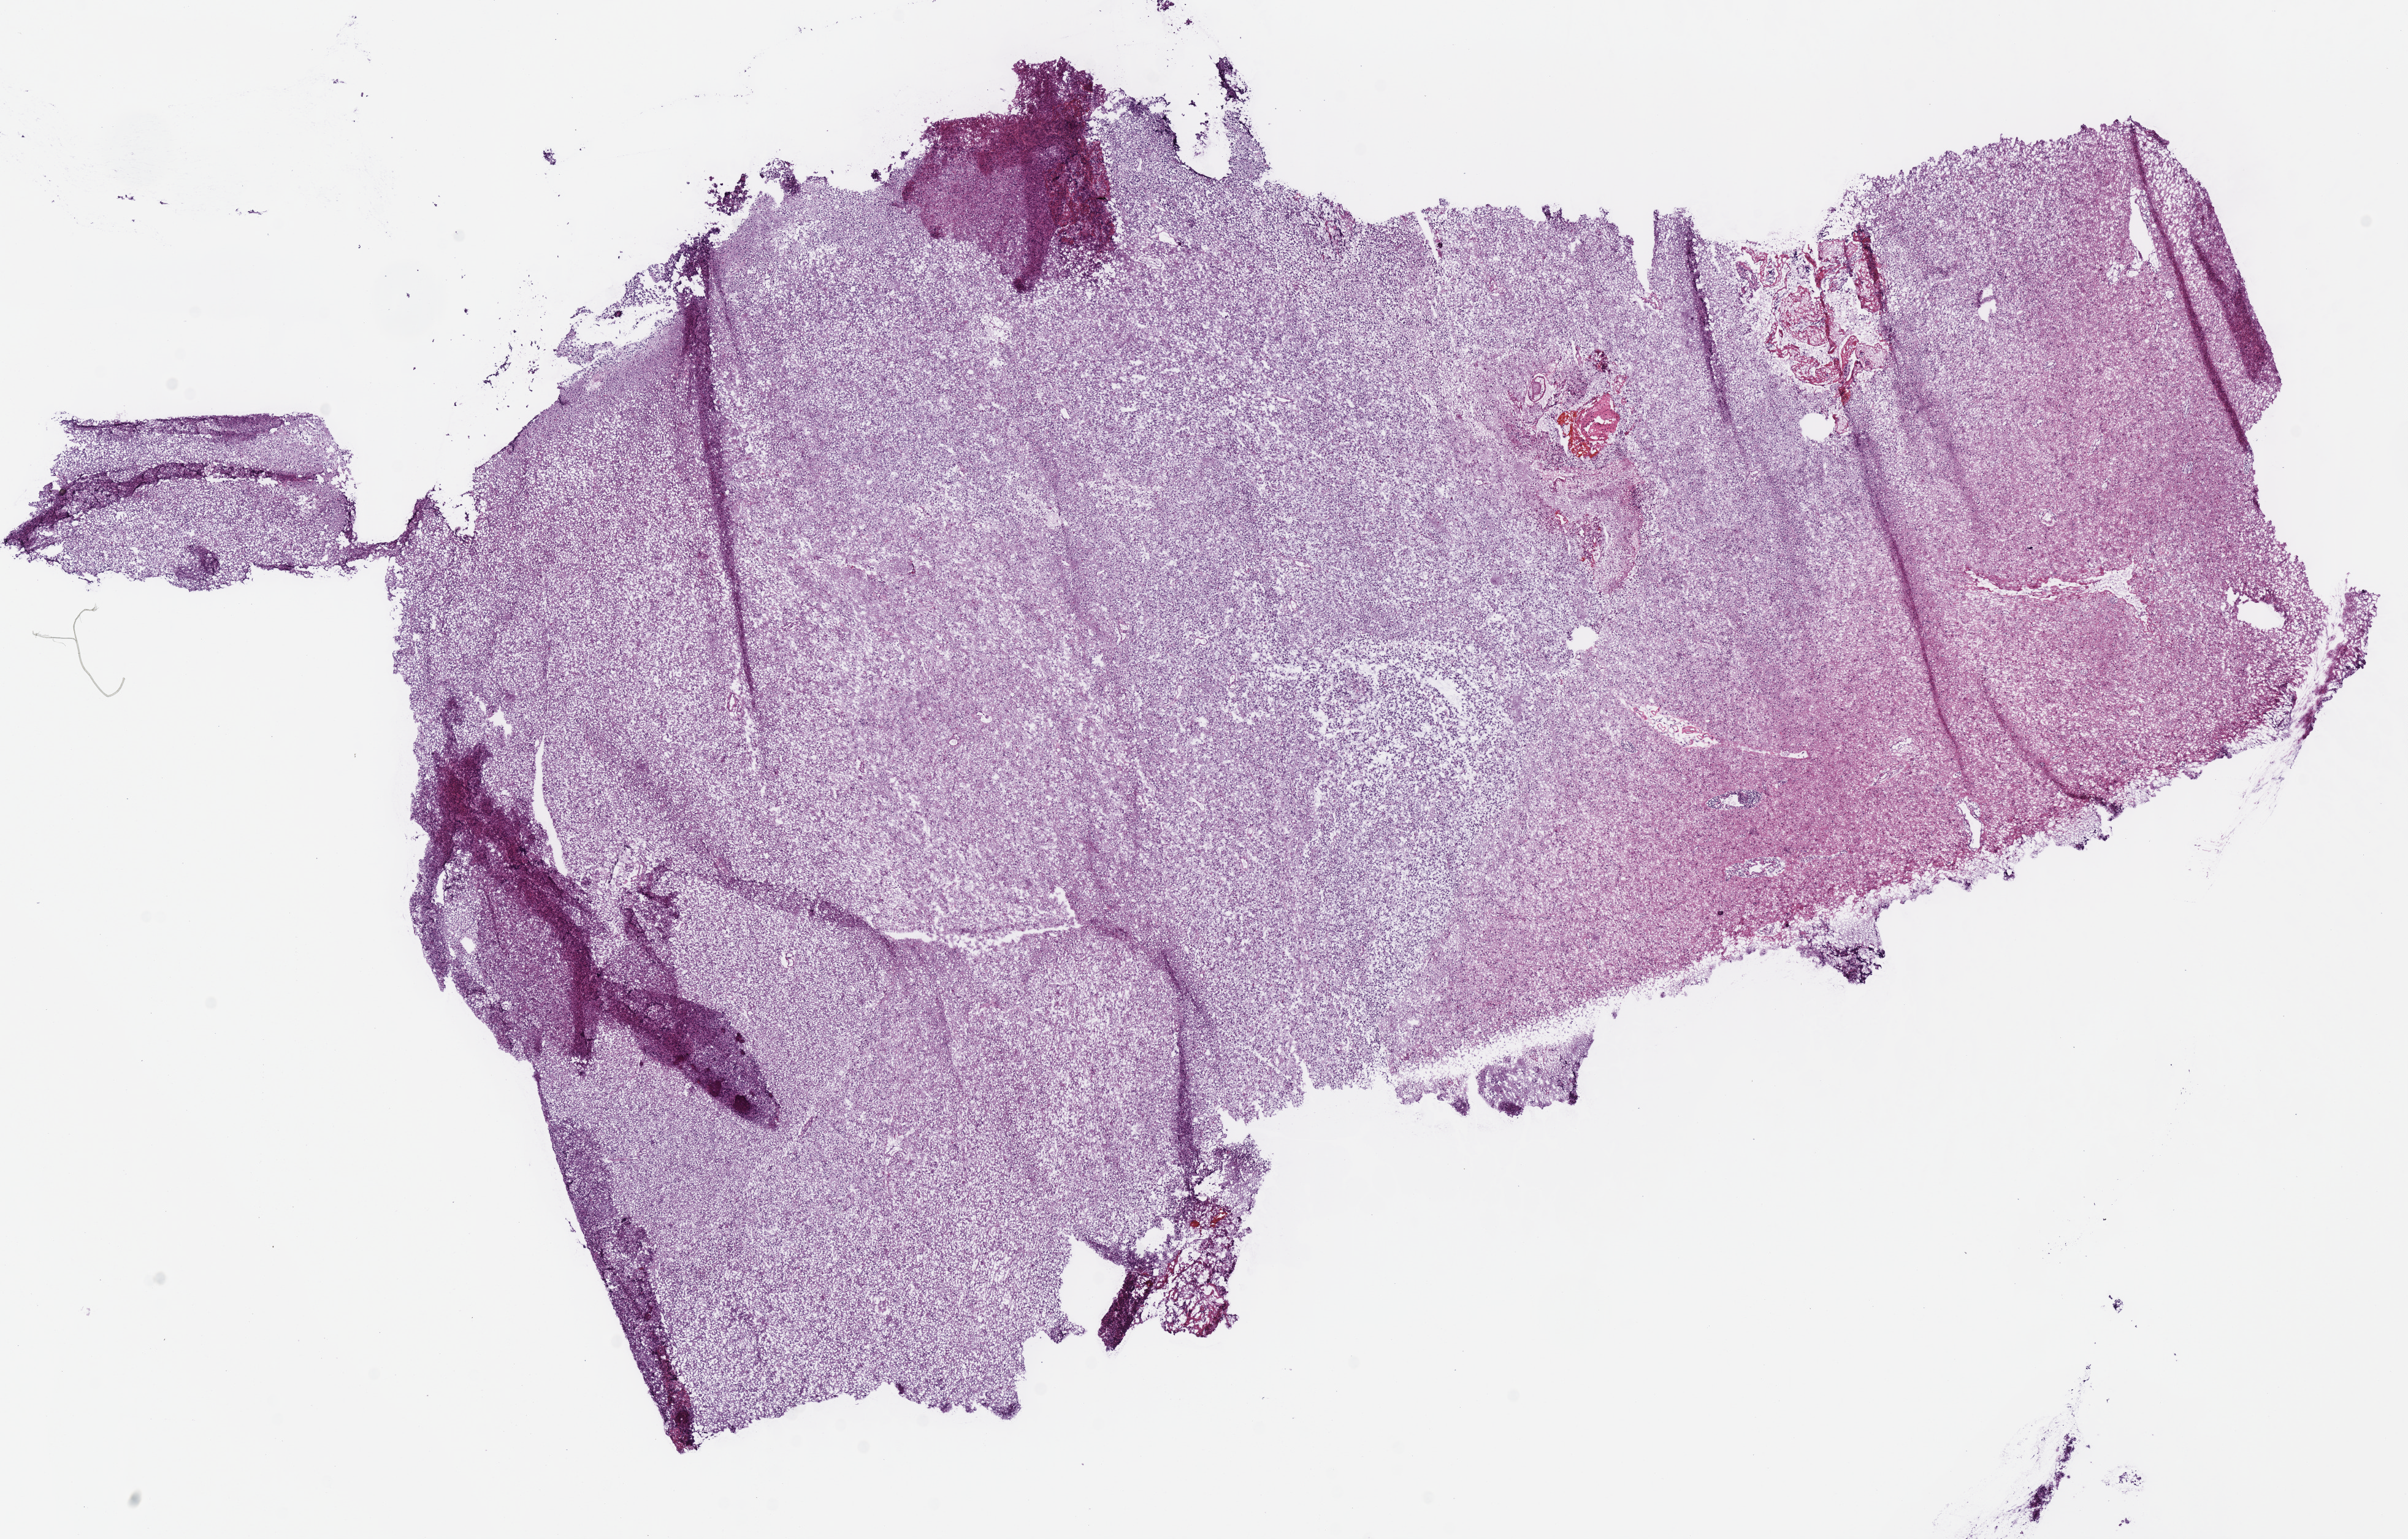
H&E-stained whole-slide image, whole scanned area (about 15.5 x 9.9 mm, from a 40x scan) shown as a low-resolution overview; frozen section from the top of the tissue portion; sample: primary tumour, brain. Male patient; age at initial diagnosis 74 years. Histologic grade: G3 (poorly differentiated). Slide review estimates, as recorded: tumour cells 100%, tumour nuclei 75%, normal cells 0%, stromal cells 0%, necrosis 0%.
Histologic diagnosis: Oligodendroglioma, anaplastic (cerebrum). Laterality: right.